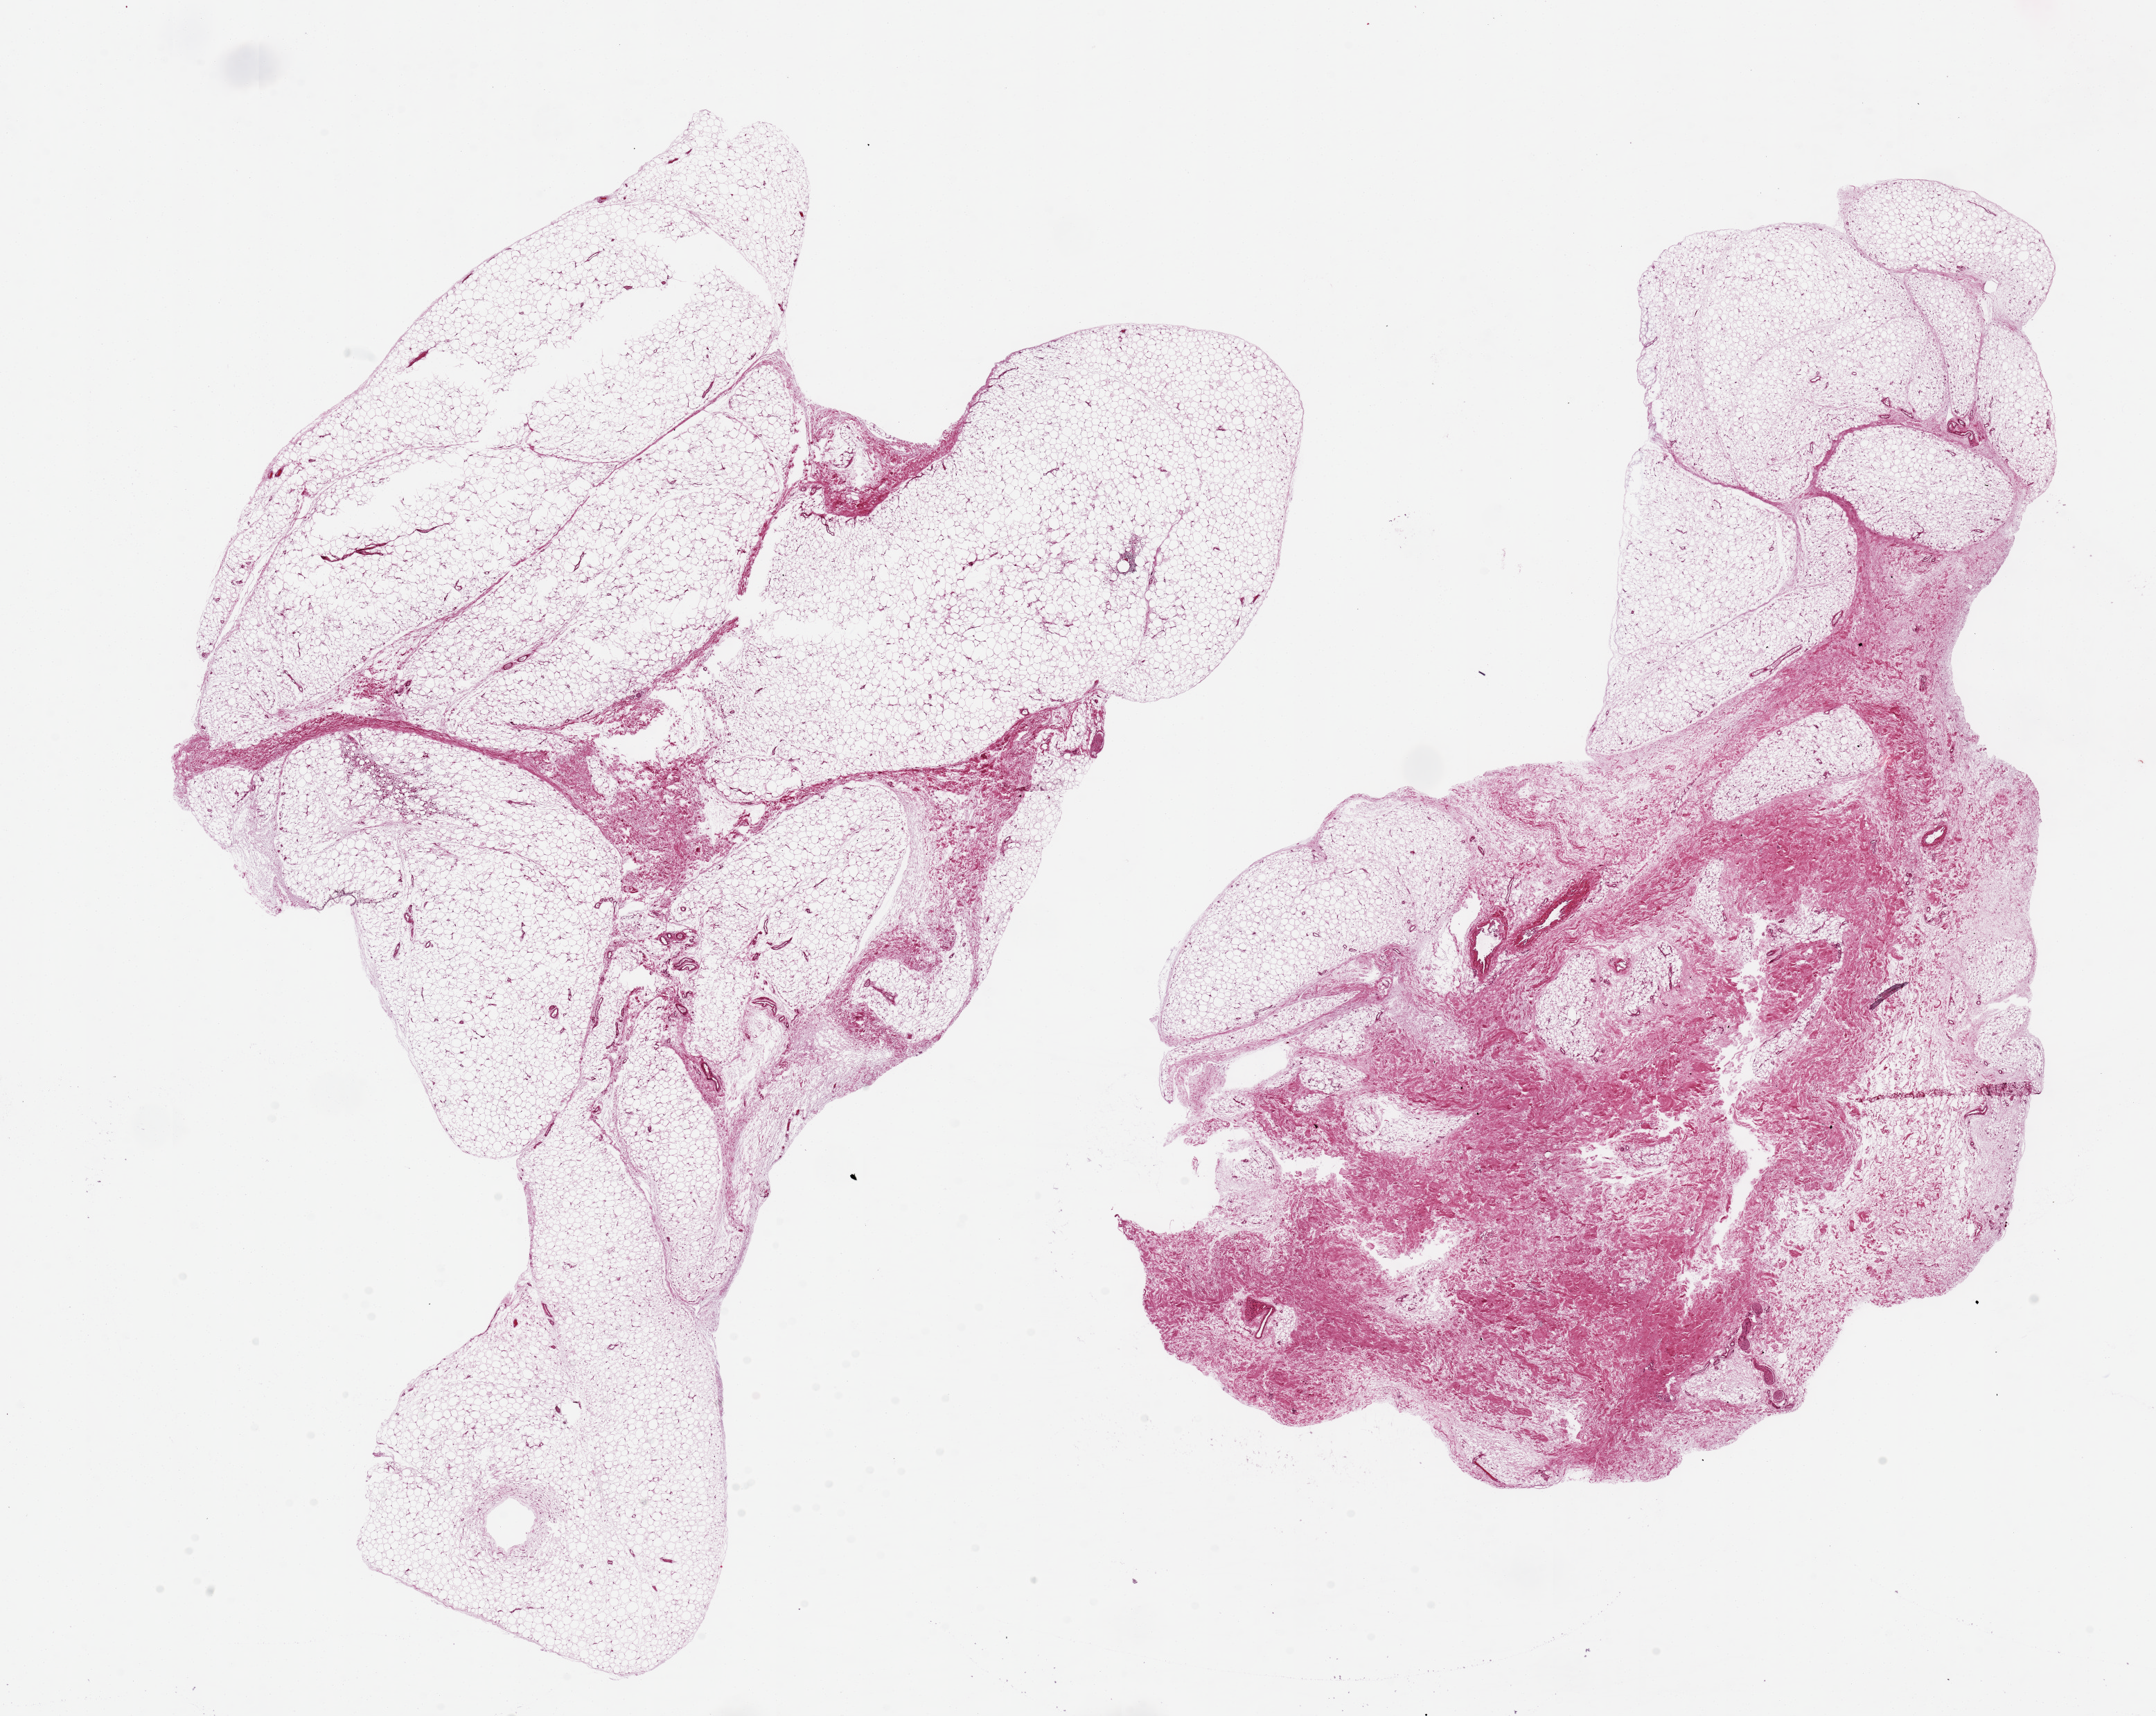
Whole-slide image, haematoxylin and eosin stain, brightfield, shown as a low-resolution overview of the whole scanned area (about 24.6 x 19.6 mm, slide scanned at 20x), PAXgene-fixed paraffin-embedded (PFPE) section, target tissue: adipose tissue, tissue donor sample.
Reviewer comment on this tissue sample: 2 pieces, 9.5x16.9 & 15.2x9.7 mm; 1 piece has a ~40% fibrous component.